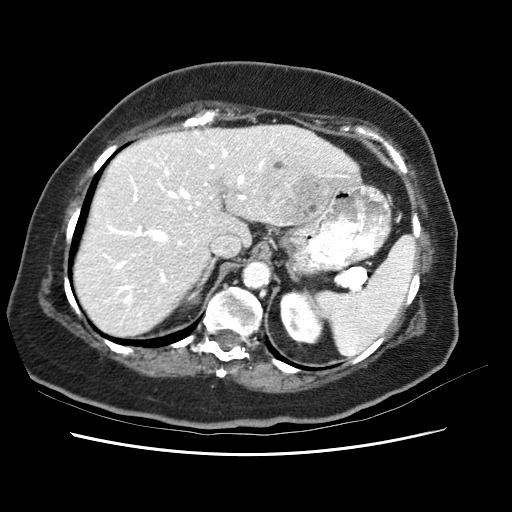
Contrast-enhanced abdominal CT (liver protocol), one axial slice. Slice 44 of 62 in the series (ordered by position). Soft-tissue window (W 400 / L 40 HU). 2.5 mm slice thickness. 512 × 512 image matrix, field of view 340 × 340 mm. Case-level facts recorded for this patient, not image findings: diagnosis: hepatocellular carcinoma (patient treated with transarterial chemoembolisation; whether this scan precedes or follows treatment is not stated here); TNM stage (as recorded): Stage-I.
Annotated regions visible in this slice (semi-automatic segmentation, software-assisted and operator-edited):
- liver parenchyma outside the tumour (the mass and vessels are separate outlines, so this box may not span the whole liver): box from (x=78, y=123) to (x=358, y=330) px
- mass: (x=256, y=143)–(x=333, y=221)
- liver vessels: (x=102, y=137)–(x=336, y=314)